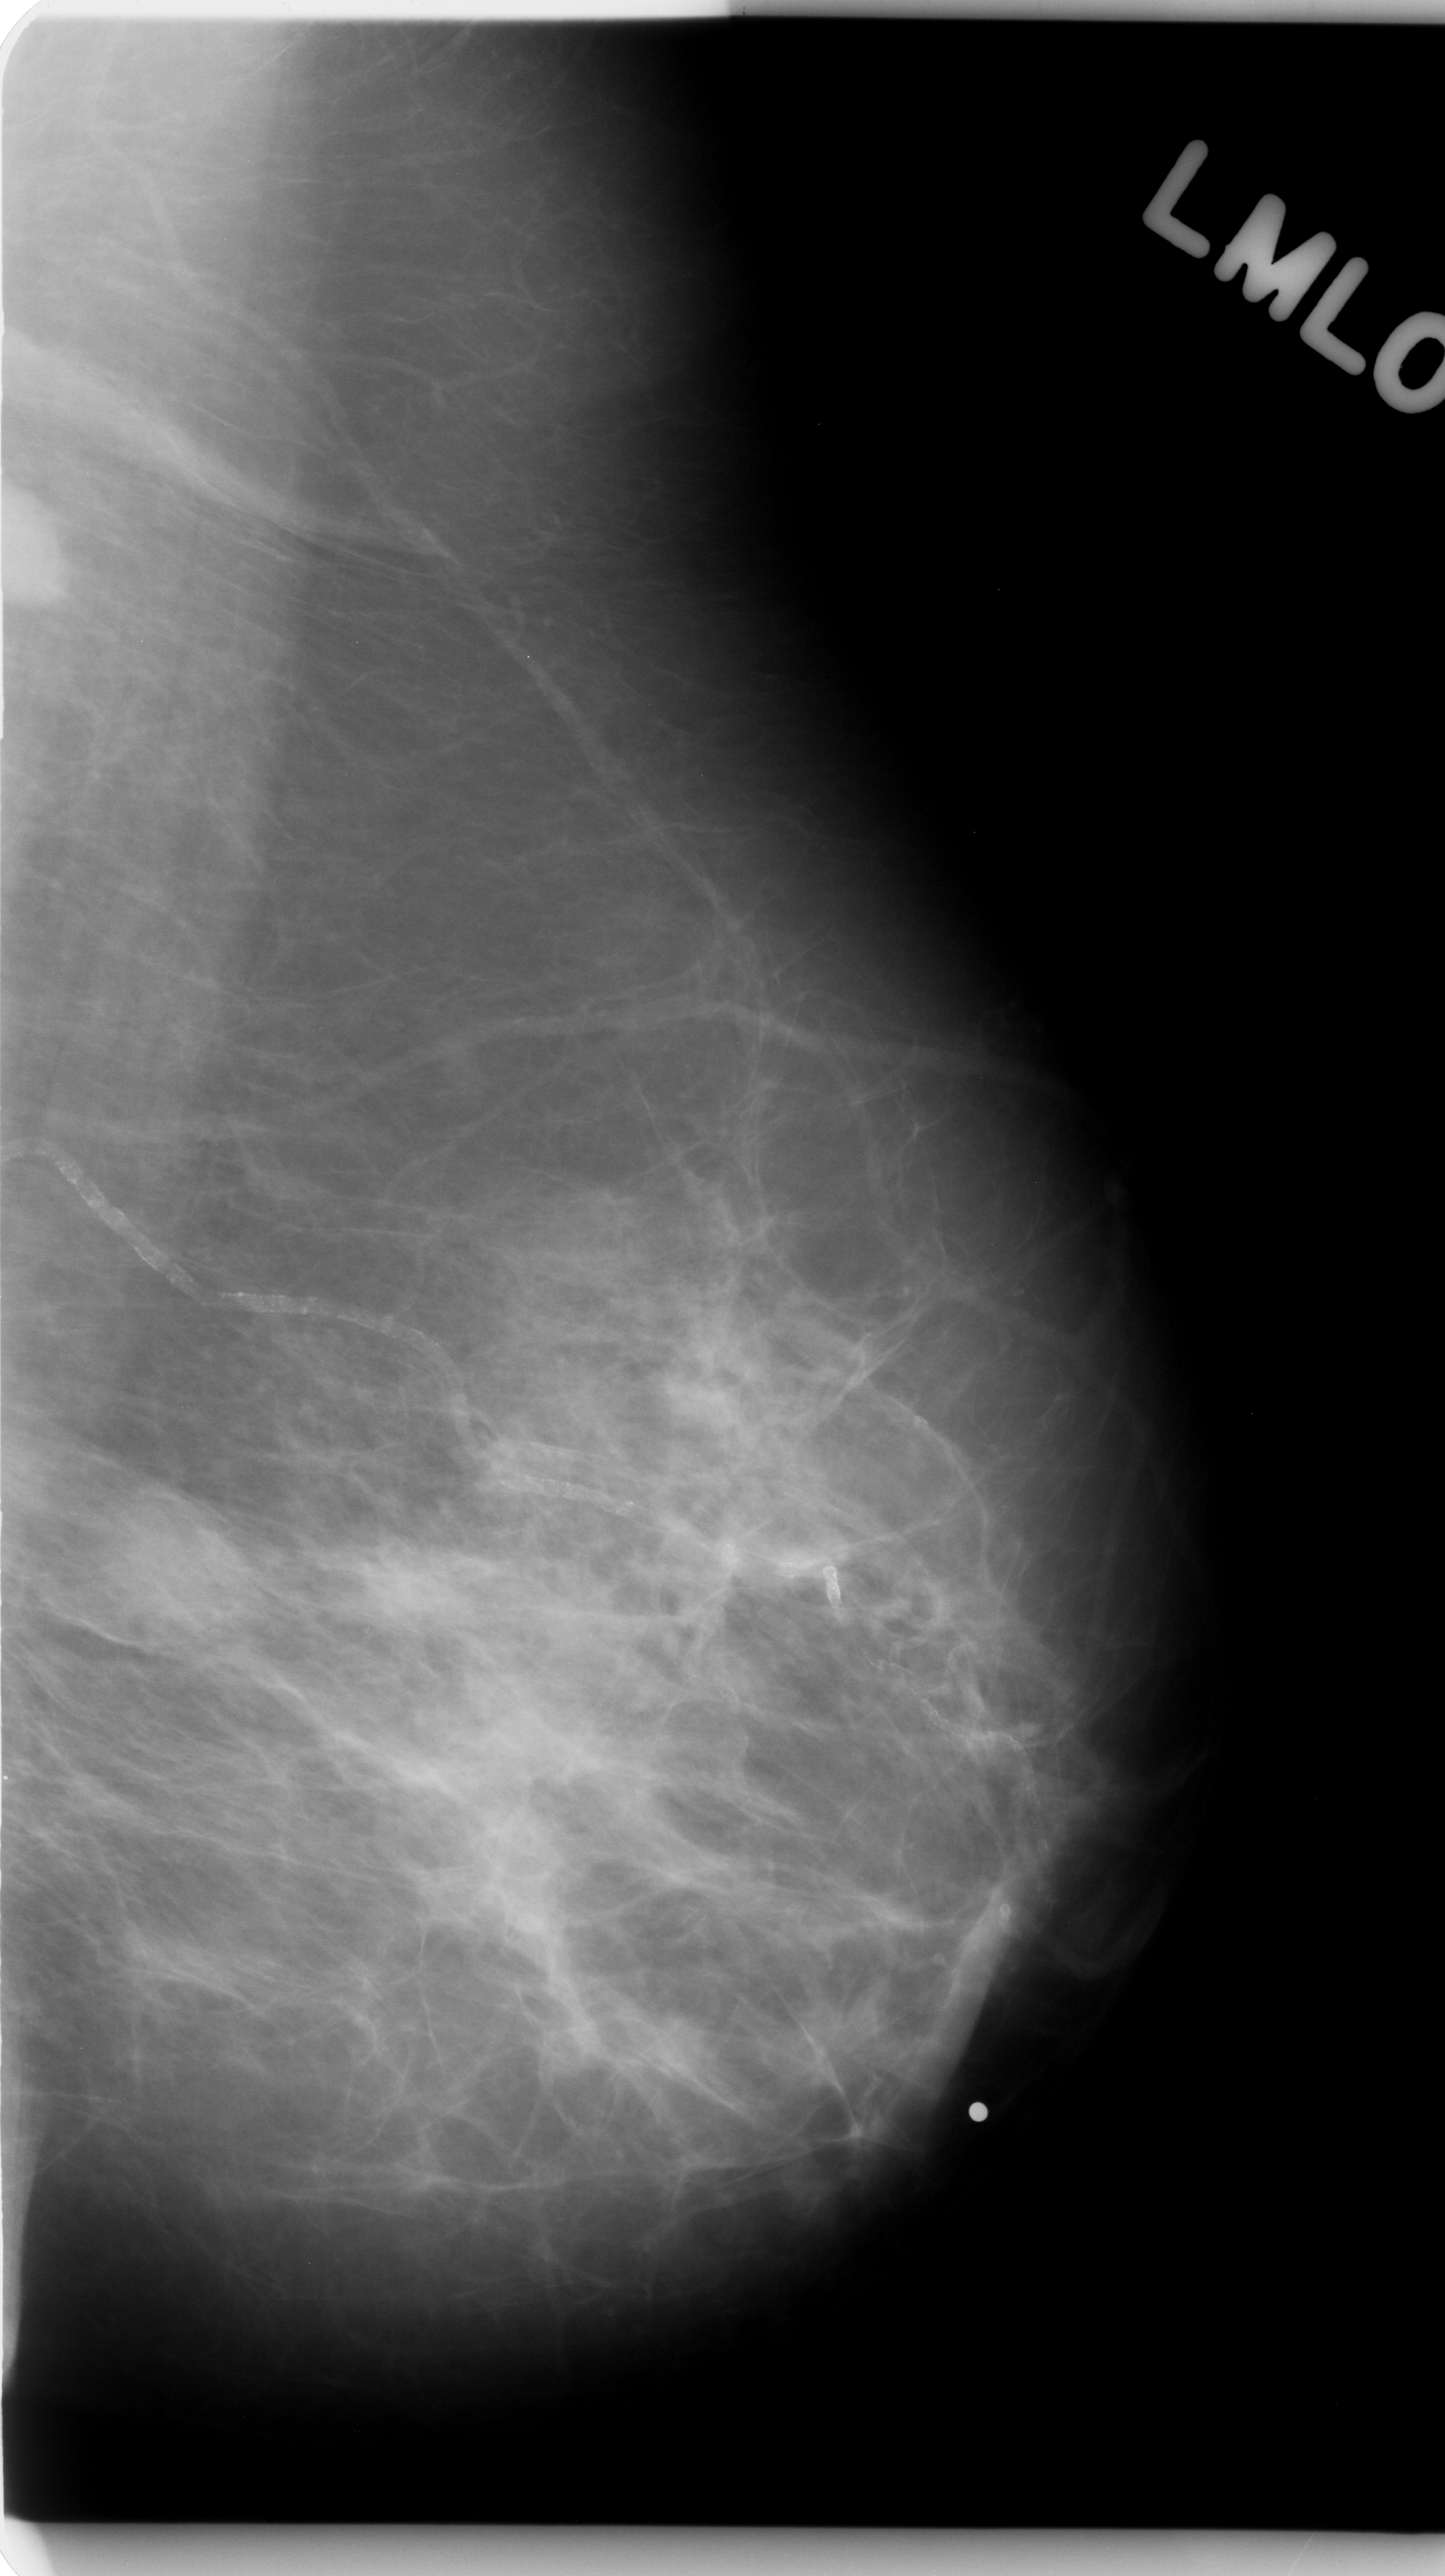
Scanned film-screen mammogram, left breast, MLO view, BI-RADS breast density category 2 (scale 1–4).
- Radiologist-marked abnormalities on this image: Finding 1 of 3: mass, shape oval, margins circumscribed; BI-RADS assessment category 5; pathology (as recorded): malignant.
- Finding 2 of 3: mass, shape lobulated, margins ill defined; BI-RADS assessment category 4; pathology (as recorded): malignant.
- Finding 3 of 3: mass, shape irregular, margins ill defined; BI-RADS assessment category 5; pathology (as recorded): malignant.